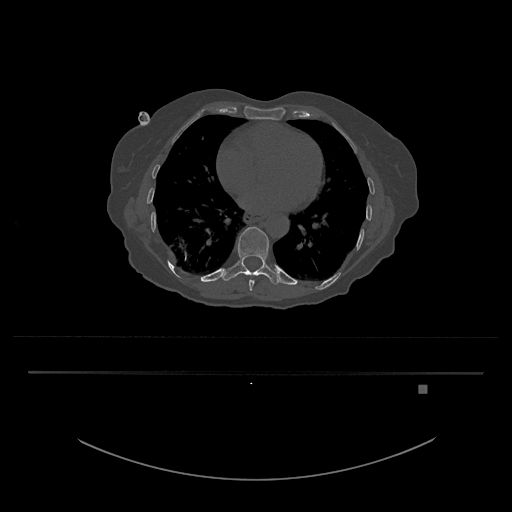
CT including the spine, one axial slice; slice 726 of 797 in the series (ordered by position); reconstruction kernel Br40s/3; 120 kVp; bone window (W 1800 / L 400 HU); 0.5 mm slice thickness; 512 × 512 image matrix, field of view 500 × 500 mm. Female patient, age 57 years. From the clinical record (not read from this slice): primary cancer: cervical.
Structures marked on this image (semi-automatic segmentation, software-assisted and operator-edited):
- T10 vertebra: box from (x=222, y=227) to (x=283, y=285) px
- T9 vertebra: (x=249, y=280)–(x=255, y=291)